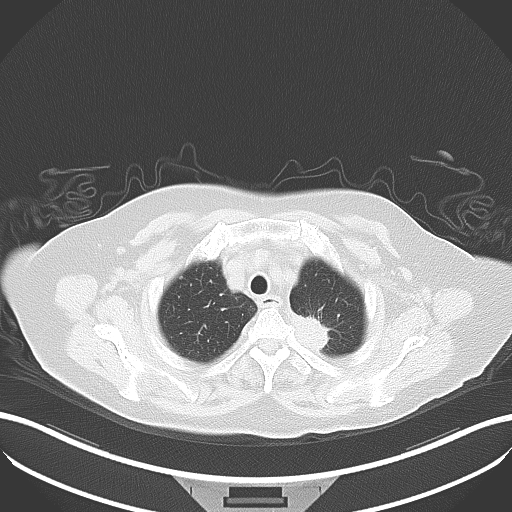
Chest CT, one axial slice; slice 35 of 42 in the series (ordered by position); 100 kVp; lung window (W 1500 / L -600 HU); 512 × 512 image matrix, field of view 400 × 400 mm. Patient: female, 81 years. From the clinical record (not read from this slice): clinical TNM (as recorded): T2a N0 M0.
Annotated regions visible in this slice (bounding box drawn by a radiologist):
- lung tumour (recorded histology: adenocarcinoma): bounding box (x1, y1, x2, y2) in pixels: (291, 308, 342, 367)